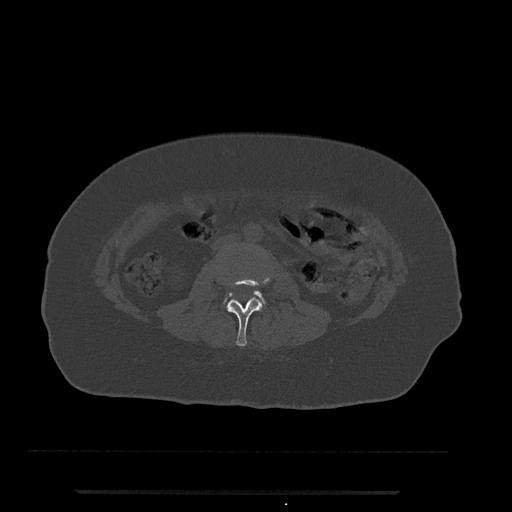
CT including the spine, one axial slice. Slice 10 of 797 in the series (ordered by position). Bone window (W 1800 / L 400 HU). 0.5 mm slice thickness. 512 × 512 image matrix, field of view 440 × 440 mm. Female patient, age 51 years. From the clinical record (not read from this slice): primary cancer: neuro.
Outlined on this slice (semi-automatic segmentation, software-assisted and operator-edited):
- L2 vertebra: bounding box [x1, y1, x2, y2] px = [226, 272, 271, 347]